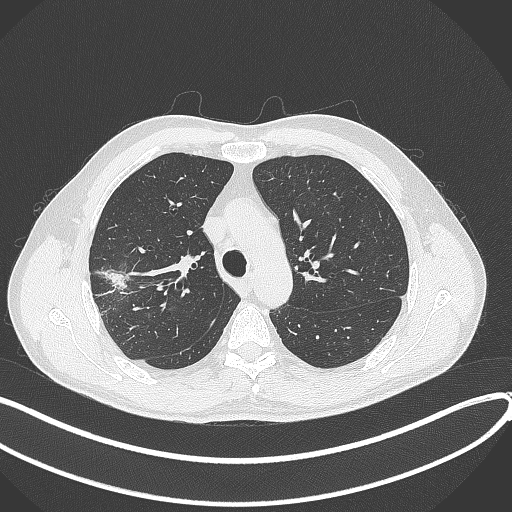
Chest CT, one axial slice; 120 kVp; lung window (W 1500 / L -600 HU); 512 × 512 image matrix. Patient: male, 62 years. From the clinical record (not read from this slice): clinical TNM (as recorded): T1c N0 M0.
Outlined on this slice (bounding box drawn by a radiologist):
- lung tumour (recorded histology: adenocarcinoma): box from (x=96, y=267) to (x=130, y=293) px